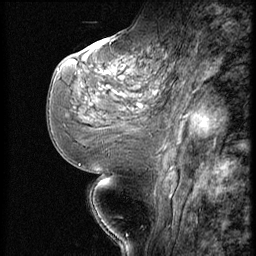
Breast MRI (dynamic contrast-enhanced), one sagittal slice. Slice 26 of 56 in the series (ordered by position). Dynamic contrast-enhanced series, image 2 of 3 at this slice position (ordered by acquisition). 1.5 T. TE 4.2 ms, TR 9 ms. 2.5 mm slice thickness. 256 × 256 image matrix. Female patient, age 51 years. From the clinical record (not read from this slice): setting: breast cancer imaged before/during neoadjuvant chemotherapy; receptor status: triple-negative.
Annotated regions visible in this slice (semi-automatic segmentation, software-assisted and operator-edited):
- analysis volume of interest (the breast-tissue region the enhancement analysis was run in; not a lesion): bounding box [x1, y1, x2, y2] px = [73, 46, 172, 147]
- tumour enhancement mask (voxels above the 140 % enhancement threshold inside the analysis volume of interest): [107, 72, 110, 75]